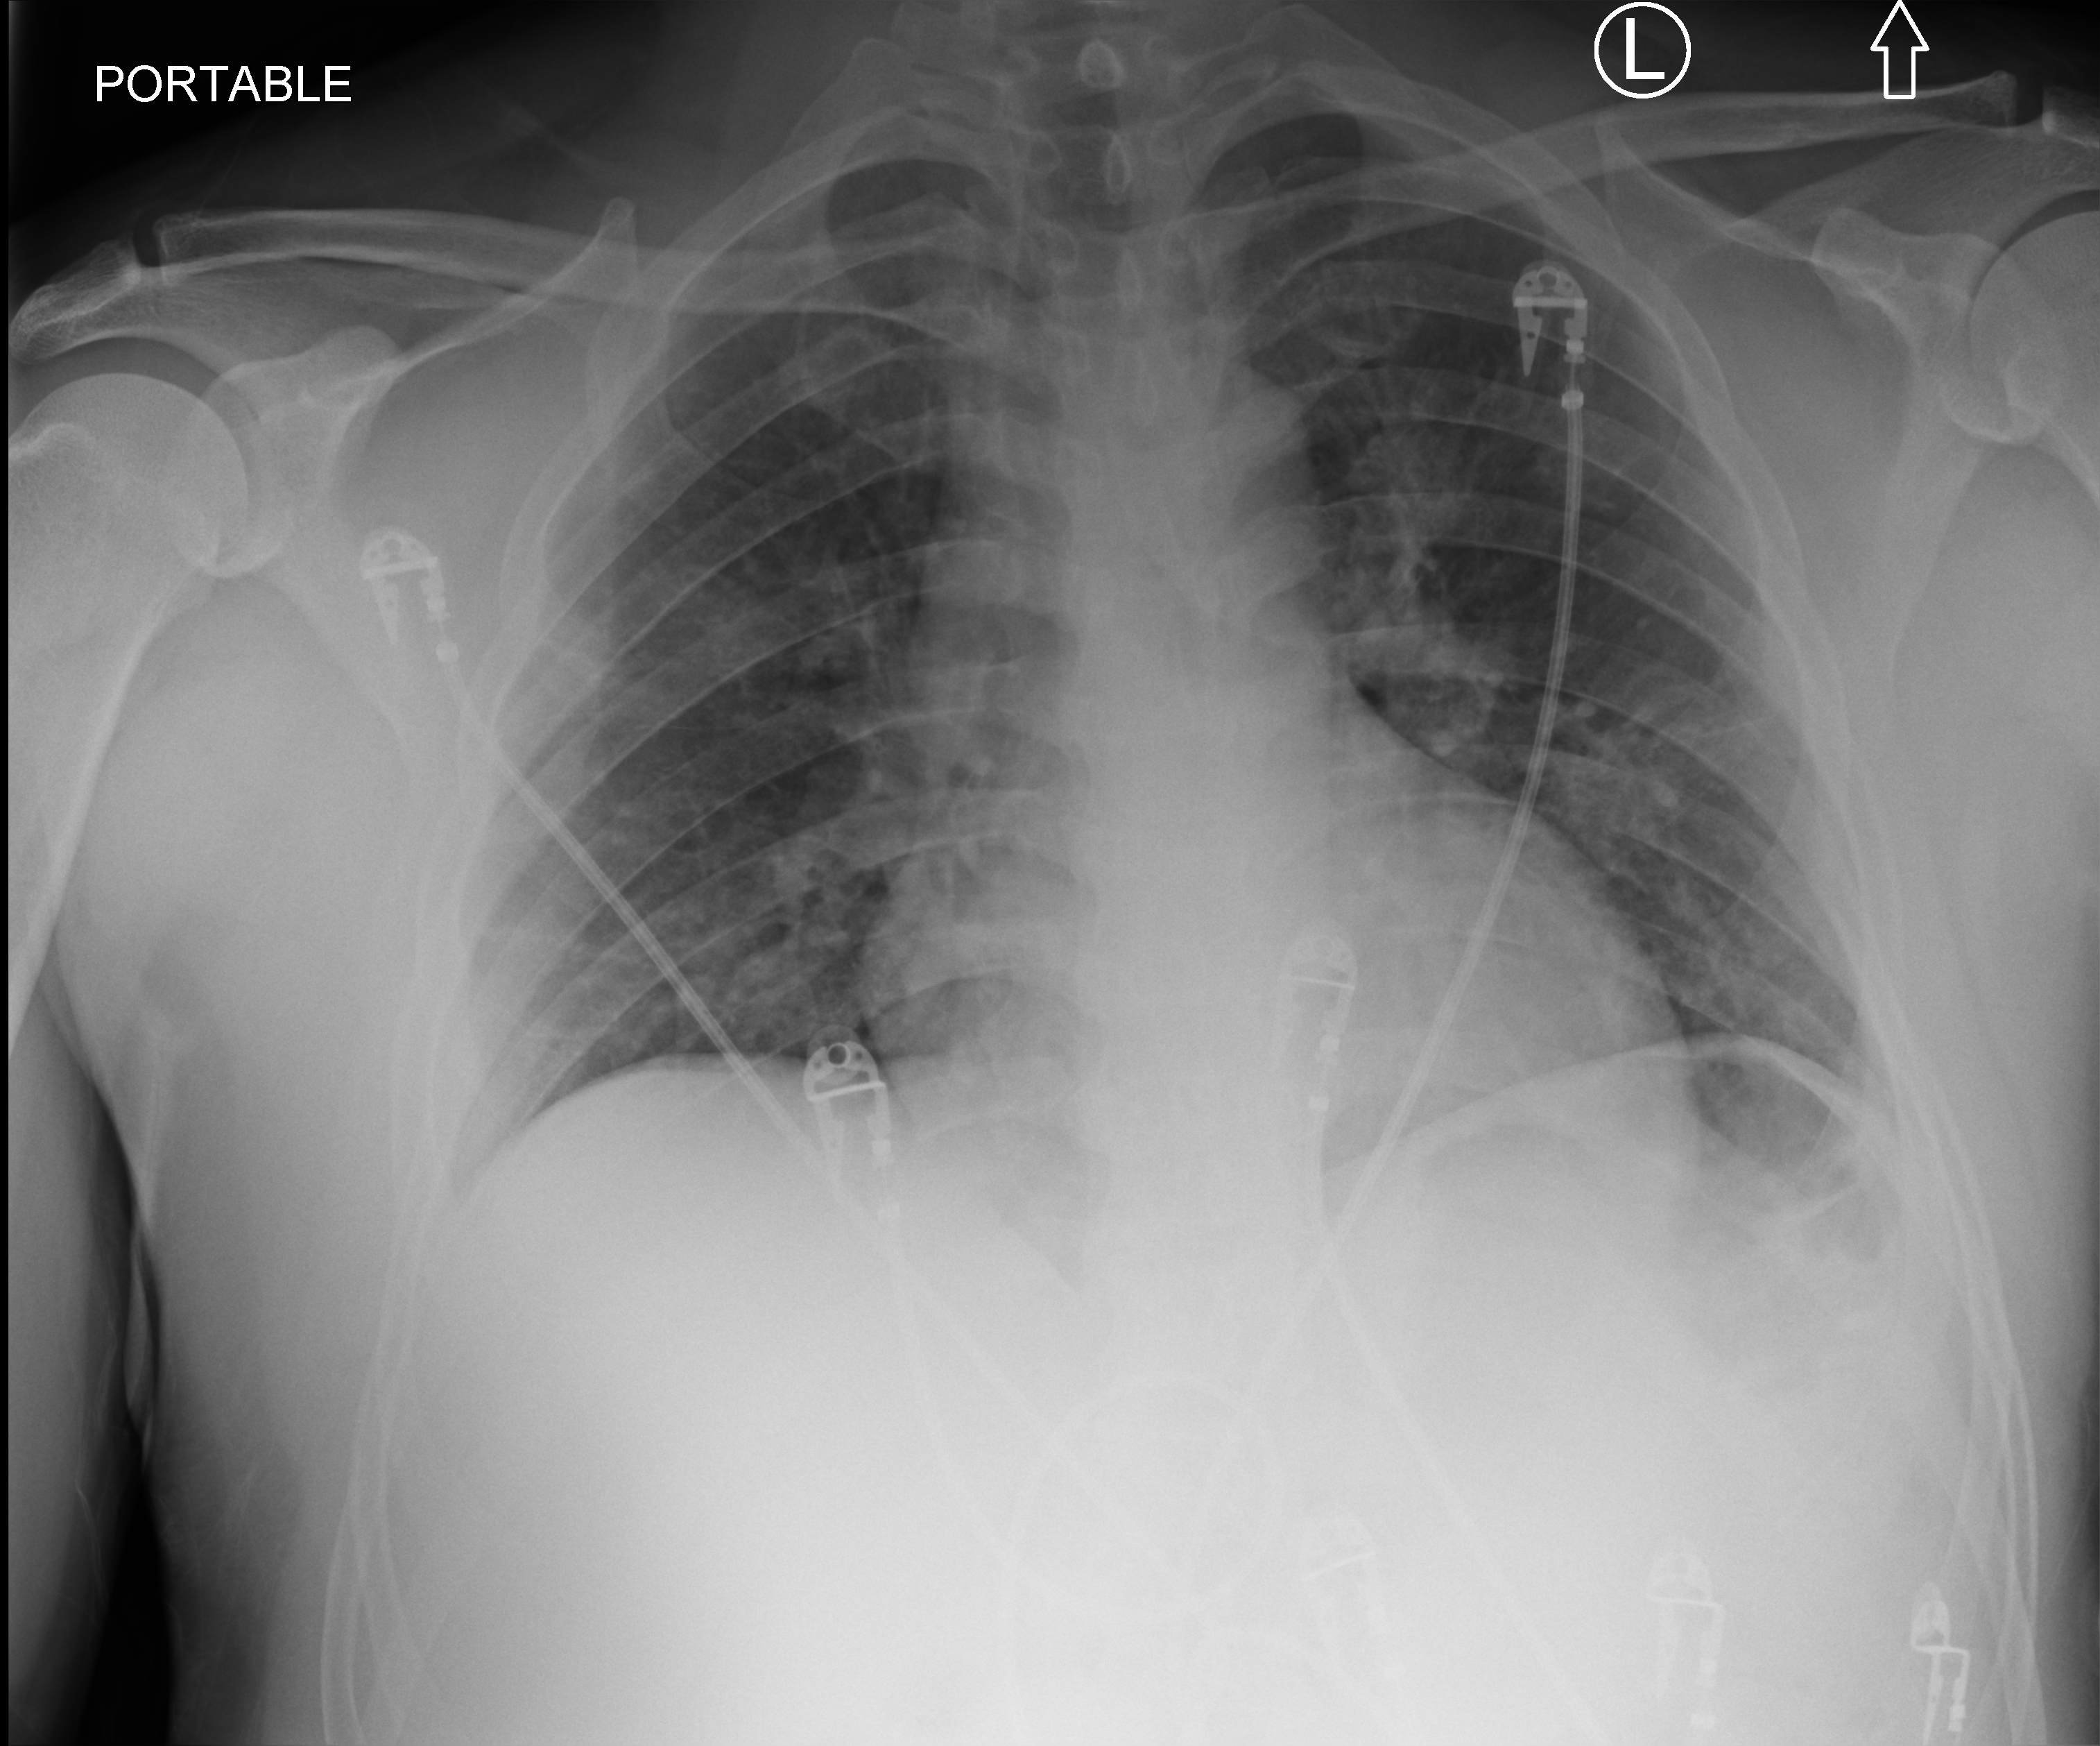
Bedside chest radiograph (computed radiography), anteroposterior (AP) projection. Patient hospitalised with COVID-19; male, aged 18–59 years.
From the hospital-stay record, not from the radiograph (when in the stay this image was taken is not recorded):
- mechanically ventilated during this hospital stay: no
- admitted to intensive care during this hospital stay: no